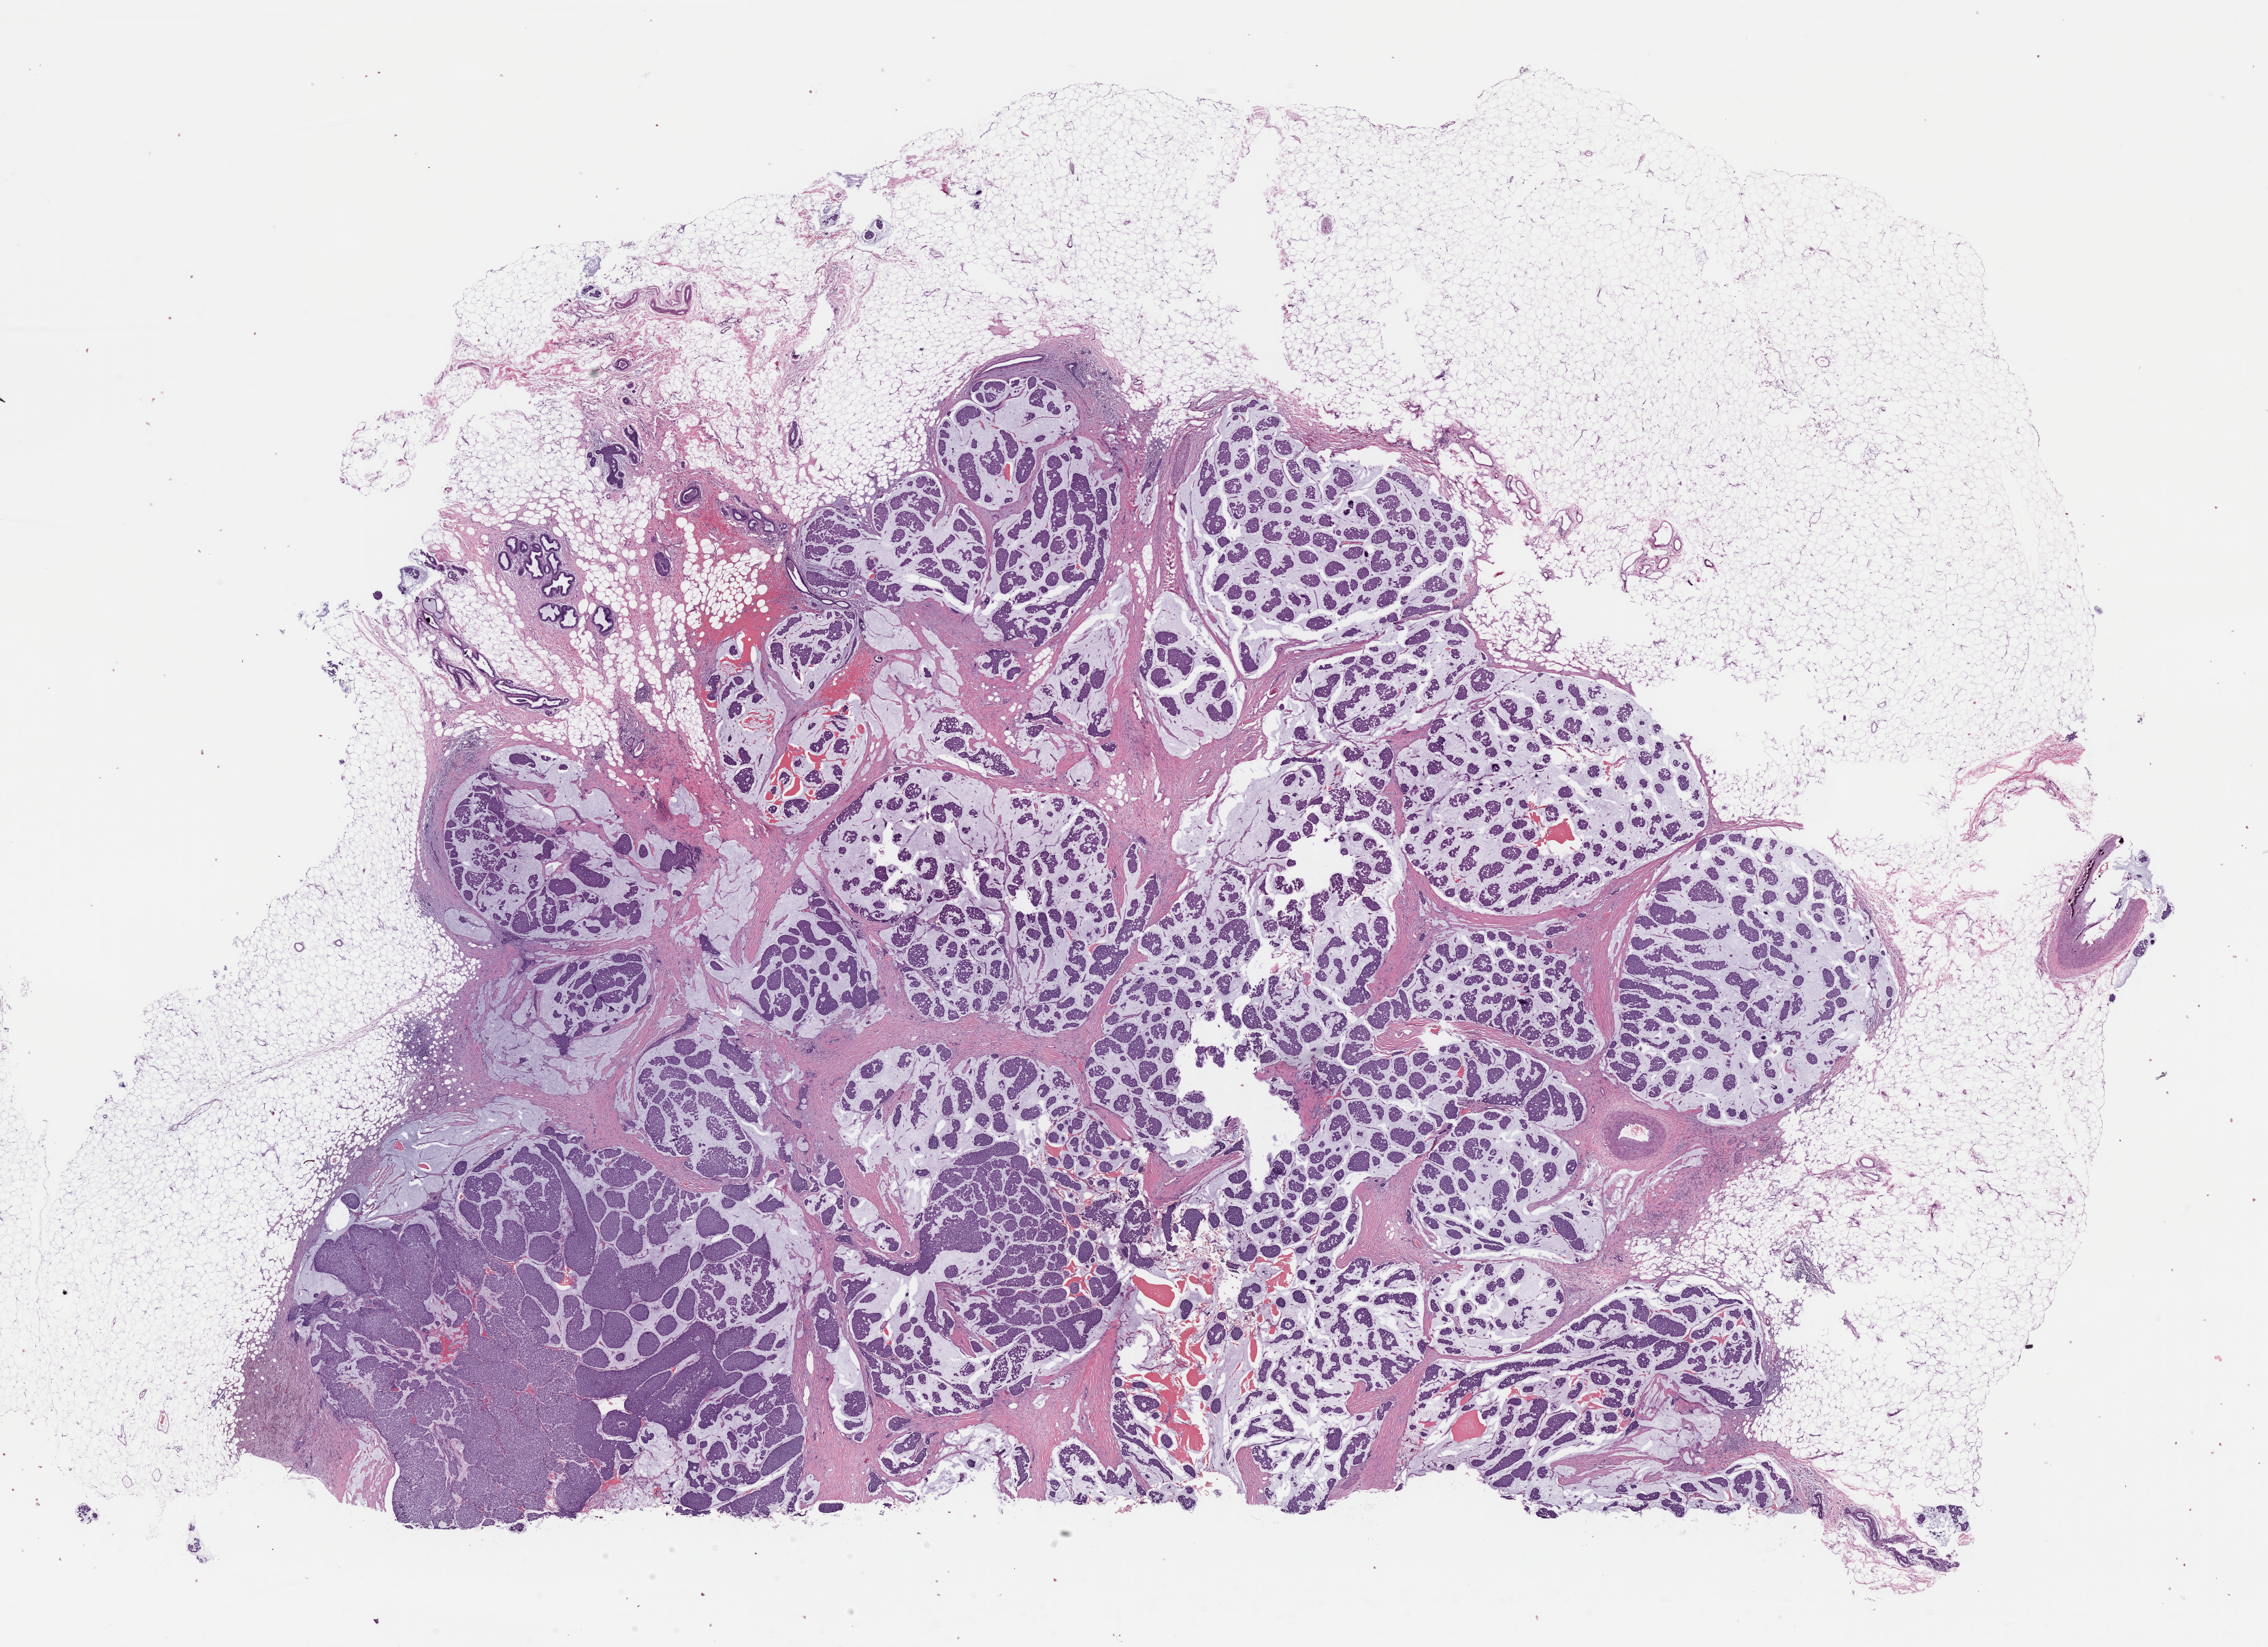
Digitized H&E-stained tissue section (whole slide) — low-resolution overview of the scanned area, about 26.3 x 19.1 mm, formalin-fixed paraffin-embedded (FFPE) diagnostic section, sample: primary tumour, breast. Female patient; age at initial diagnosis 77 years.
Histologic diagnosis: Mucinous adenocarcinoma.